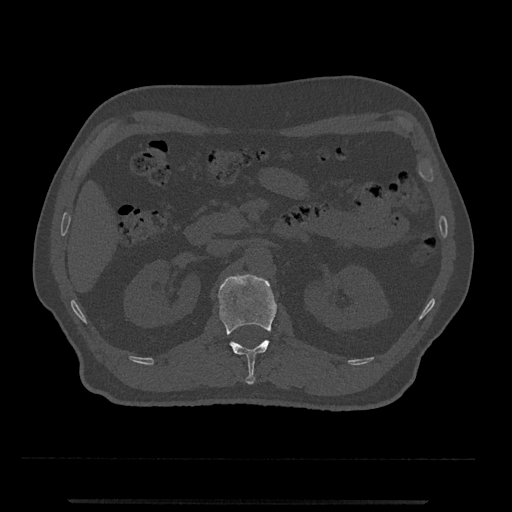
CT including the spine, one axial slice. Bone window (W 1800 / L 400 HU). 512 × 512 image matrix. Patient: male, 63 years. Case-level facts recorded for this patient, not image findings: primary cancer: prostate.
Annotated regions visible in this slice (semi-automatically segmented with operator editing):
- L1 vertebra: bounding box (x1, y1, x2, y2) in pixels: (218, 274, 277, 385)